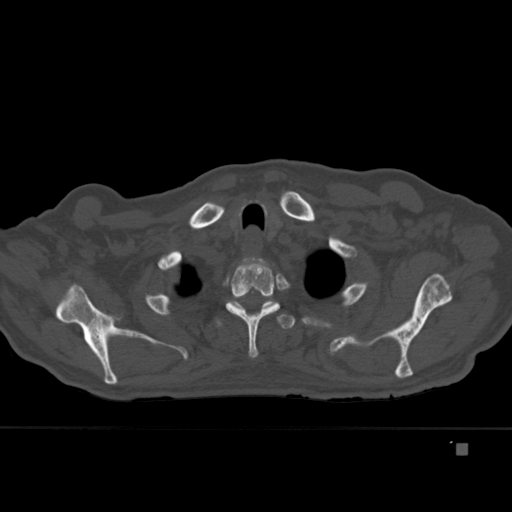
CT including the spine, one axial slice. Position 345 of 451 along the scan axis. Bone window (W 1800 / L 400 HU). 512 × 512 image matrix, field of view 378 × 378 mm. Patient: male, 75 years. Case-level facts recorded for this patient, not image findings: primary cancer: prostate.
Structures marked on this image (semi-automatically segmented with operator editing):
- T1 vertebra: bounding box <244,258,264,264> (left, top, right, bottom; pixels)
- T2 vertebra: <226,257,280,358>
- T3 vertebra: <217,300,296,329>